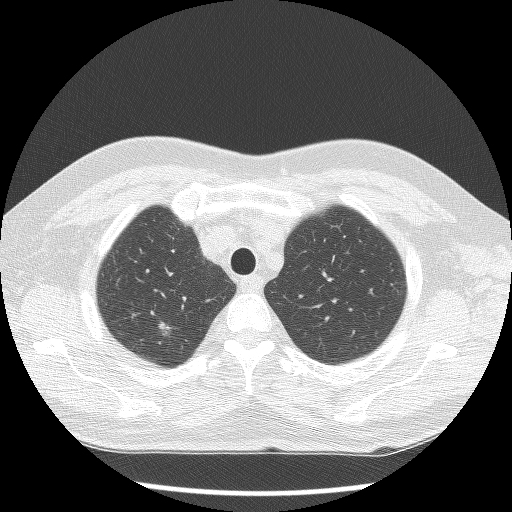
Chest CT (low-dose screening protocol), one axial image; first (baseline) screen; lung window (W 1500 / L -600 HU); 2.5 mm slice thickness; 120 kVp; slice 21 of 120 in the series. Male participant, aged 70 years at enrolment. Current smoker at enrolment.
Lesion marked by an expert reader, bounding box <128,309,192,358> (left, top, right, bottom; pixels). Screening reader's record for this exam (one nodule recorded; not confirmed to be the boxed lesion): non-calcified nodule or mass ≥4 mm, right upper lobe, 12 × 10 mm, smooth margins, soft tissue attenuation. Official screen result: positive, change unspecified: nodule(s) >= 4 mm or enlarging nodule(s), mass(es), or other non-specific abnormalities suspicious for lung cancer. Lung cancer was diagnosed 14 days after this screen: large cell neuroendocrine carcinoma, right upper lobe, poorly differentiated (G3), stage IA (AJCC 6th edition), 15 mm at pathology.